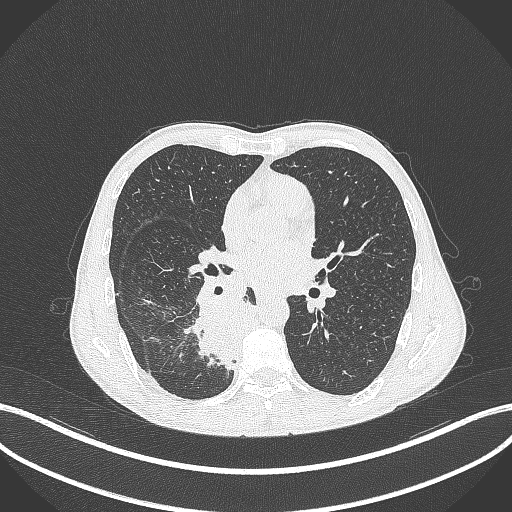
Chest CT, one axial slice; slice 190 of 371 in the series (ordered by position); reconstruction kernel B70f; 120 kVp; lung window (W 1500 / L -600 HU); 512 × 512 image matrix, field of view 400 × 400 mm. Patient: male, 58 years. Case-level facts recorded for this patient, not image findings: clinical TNM (as recorded): T3 N1 M1.
Annotated regions visible in this slice (bounding box drawn by a radiologist):
- lung tumour (recorded histology: squamous cell carcinoma): bounding box [x1, y1, x2, y2] px = [187, 287, 263, 377]